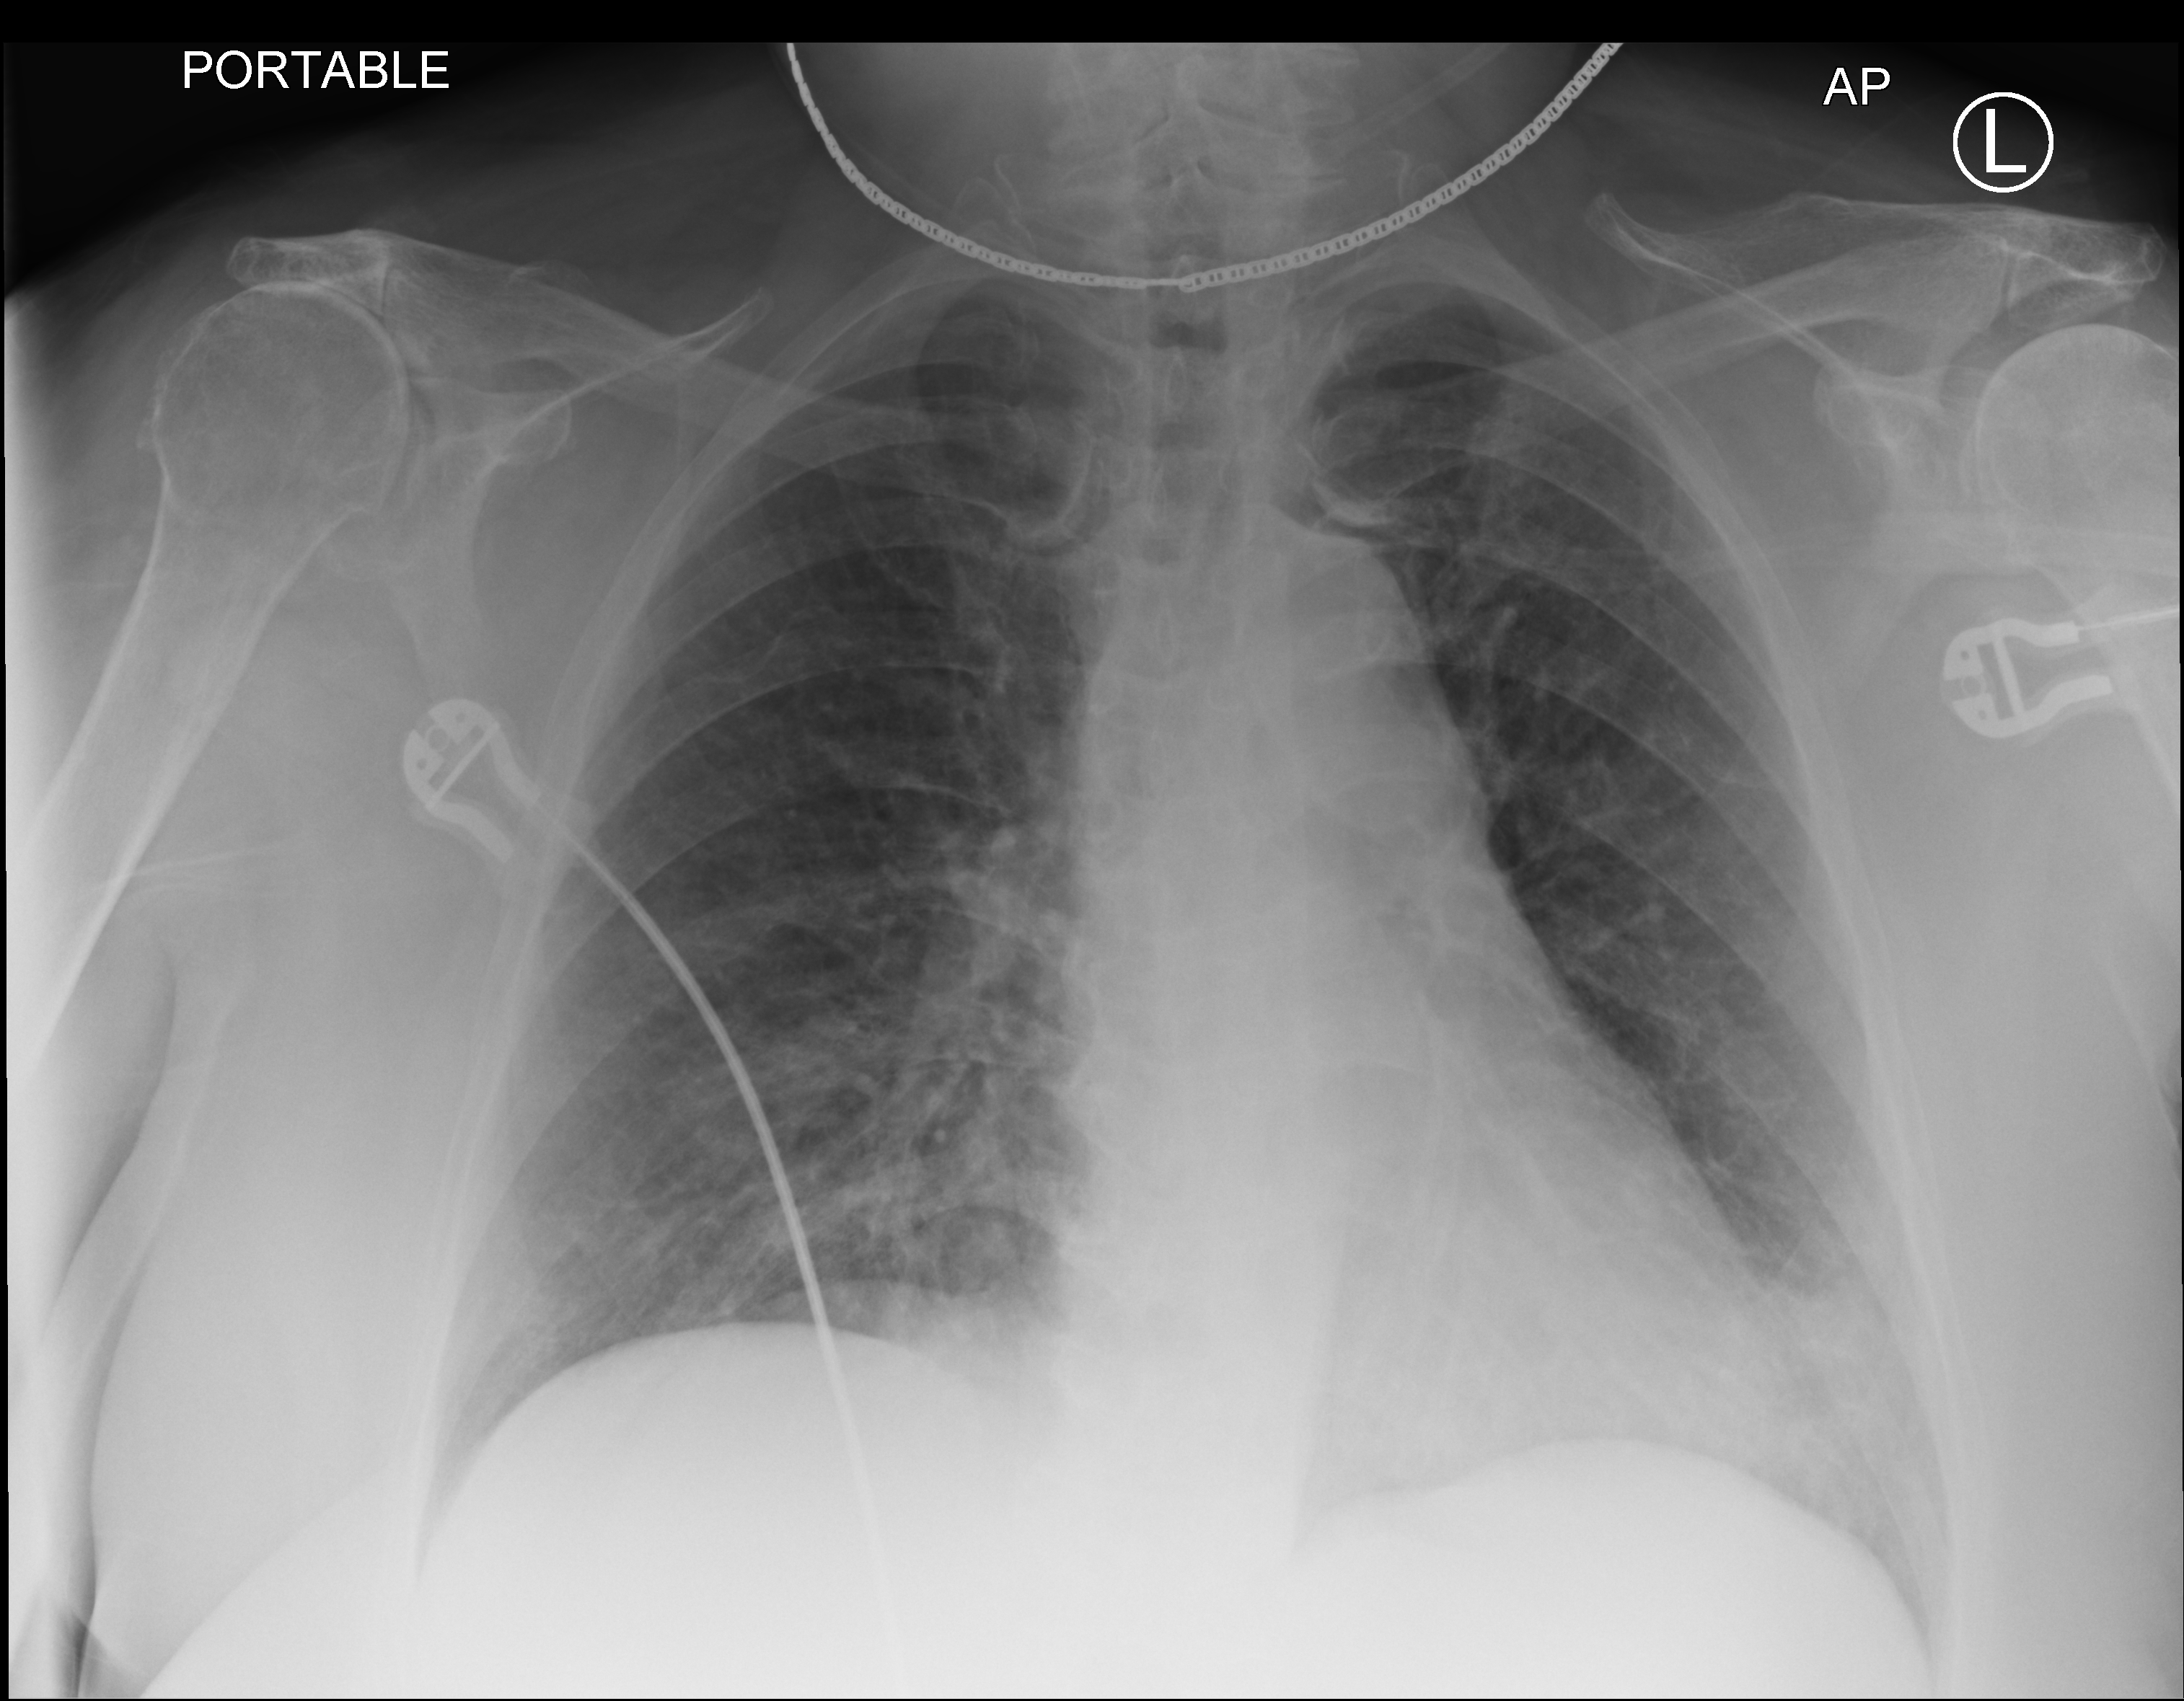
Chest X-ray (portable); anteroposterior (AP) projection. Female patient hospitalised with COVID-19, age 60–74 years.
From the hospital-stay record, not from the radiograph (when in the stay this image was taken is not recorded):
- admitted to intensive care during this hospital stay: no